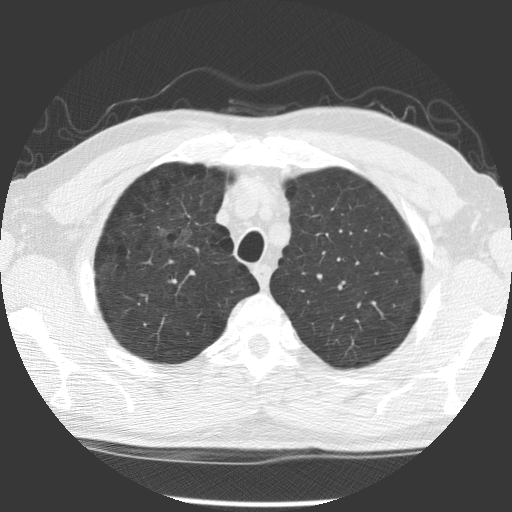
Low-dose screening chest CT, axial slice. Baseline screening round. Lung window (W 1500 / L -600 HU). 2.5 mm slice thickness. Standard (soft-tissue) reconstruction kernel (STANDARD). 140 kVp. Male, age 60 years at enrolment.
Expert-annotated lung lesion, box from (x=142, y=216) to (x=198, y=264) px. Reader record for this screening exam (exam-level; its link to the box is not recorded): non-calcified nodule or mass ≥4 mm, right middle lobe, 20 × 20 mm, poorly defined margins, ground glass attenuation. Lung cancer was diagnosed 863 days after this screen (after the third annual screen): papillary adenocarcinoma, NOS, right upper lobe, moderately differentiated (G2), stage IB (AJCC 6th edition), 32 mm at pathology.